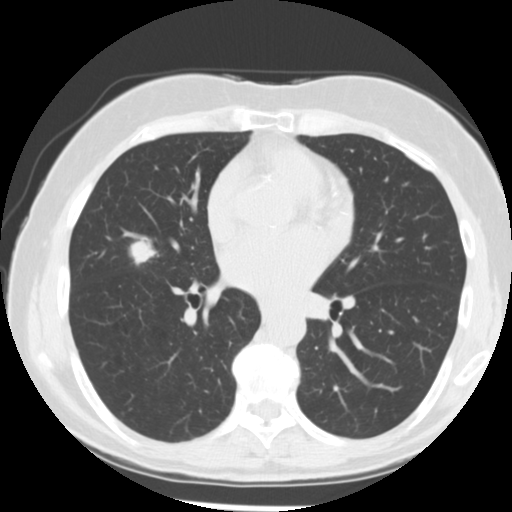
Axial slice from a low-dose chest CT screening exam, baseline annual screen, lung window (W 1500 / L -600 HU). Female participant, aged 66 years at enrolment.
• Expert-annotated lung lesion, bounding box [x1, y1, x2, y2] px = [122, 236, 163, 269].
• Screening reader's record for this exam (one nodule recorded; not confirmed to be the boxed lesion): non-calcified nodule or mass ≥4 mm, right middle lobe, 15 × 13 mm, poorly defined margins, soft tissue attenuation.
• Official screen result: positive, change unspecified: nodule(s) >= 4 mm or enlarging nodule(s), mass(es), or other non-specific abnormalities suspicious for lung cancer.
• Lung cancer was diagnosed 27 days after this screen: adenocarcinoma, NOS, right middle lobe, undifferentiated (G4), stage IIIA (AJCC 6th edition), 18 mm at pathology.